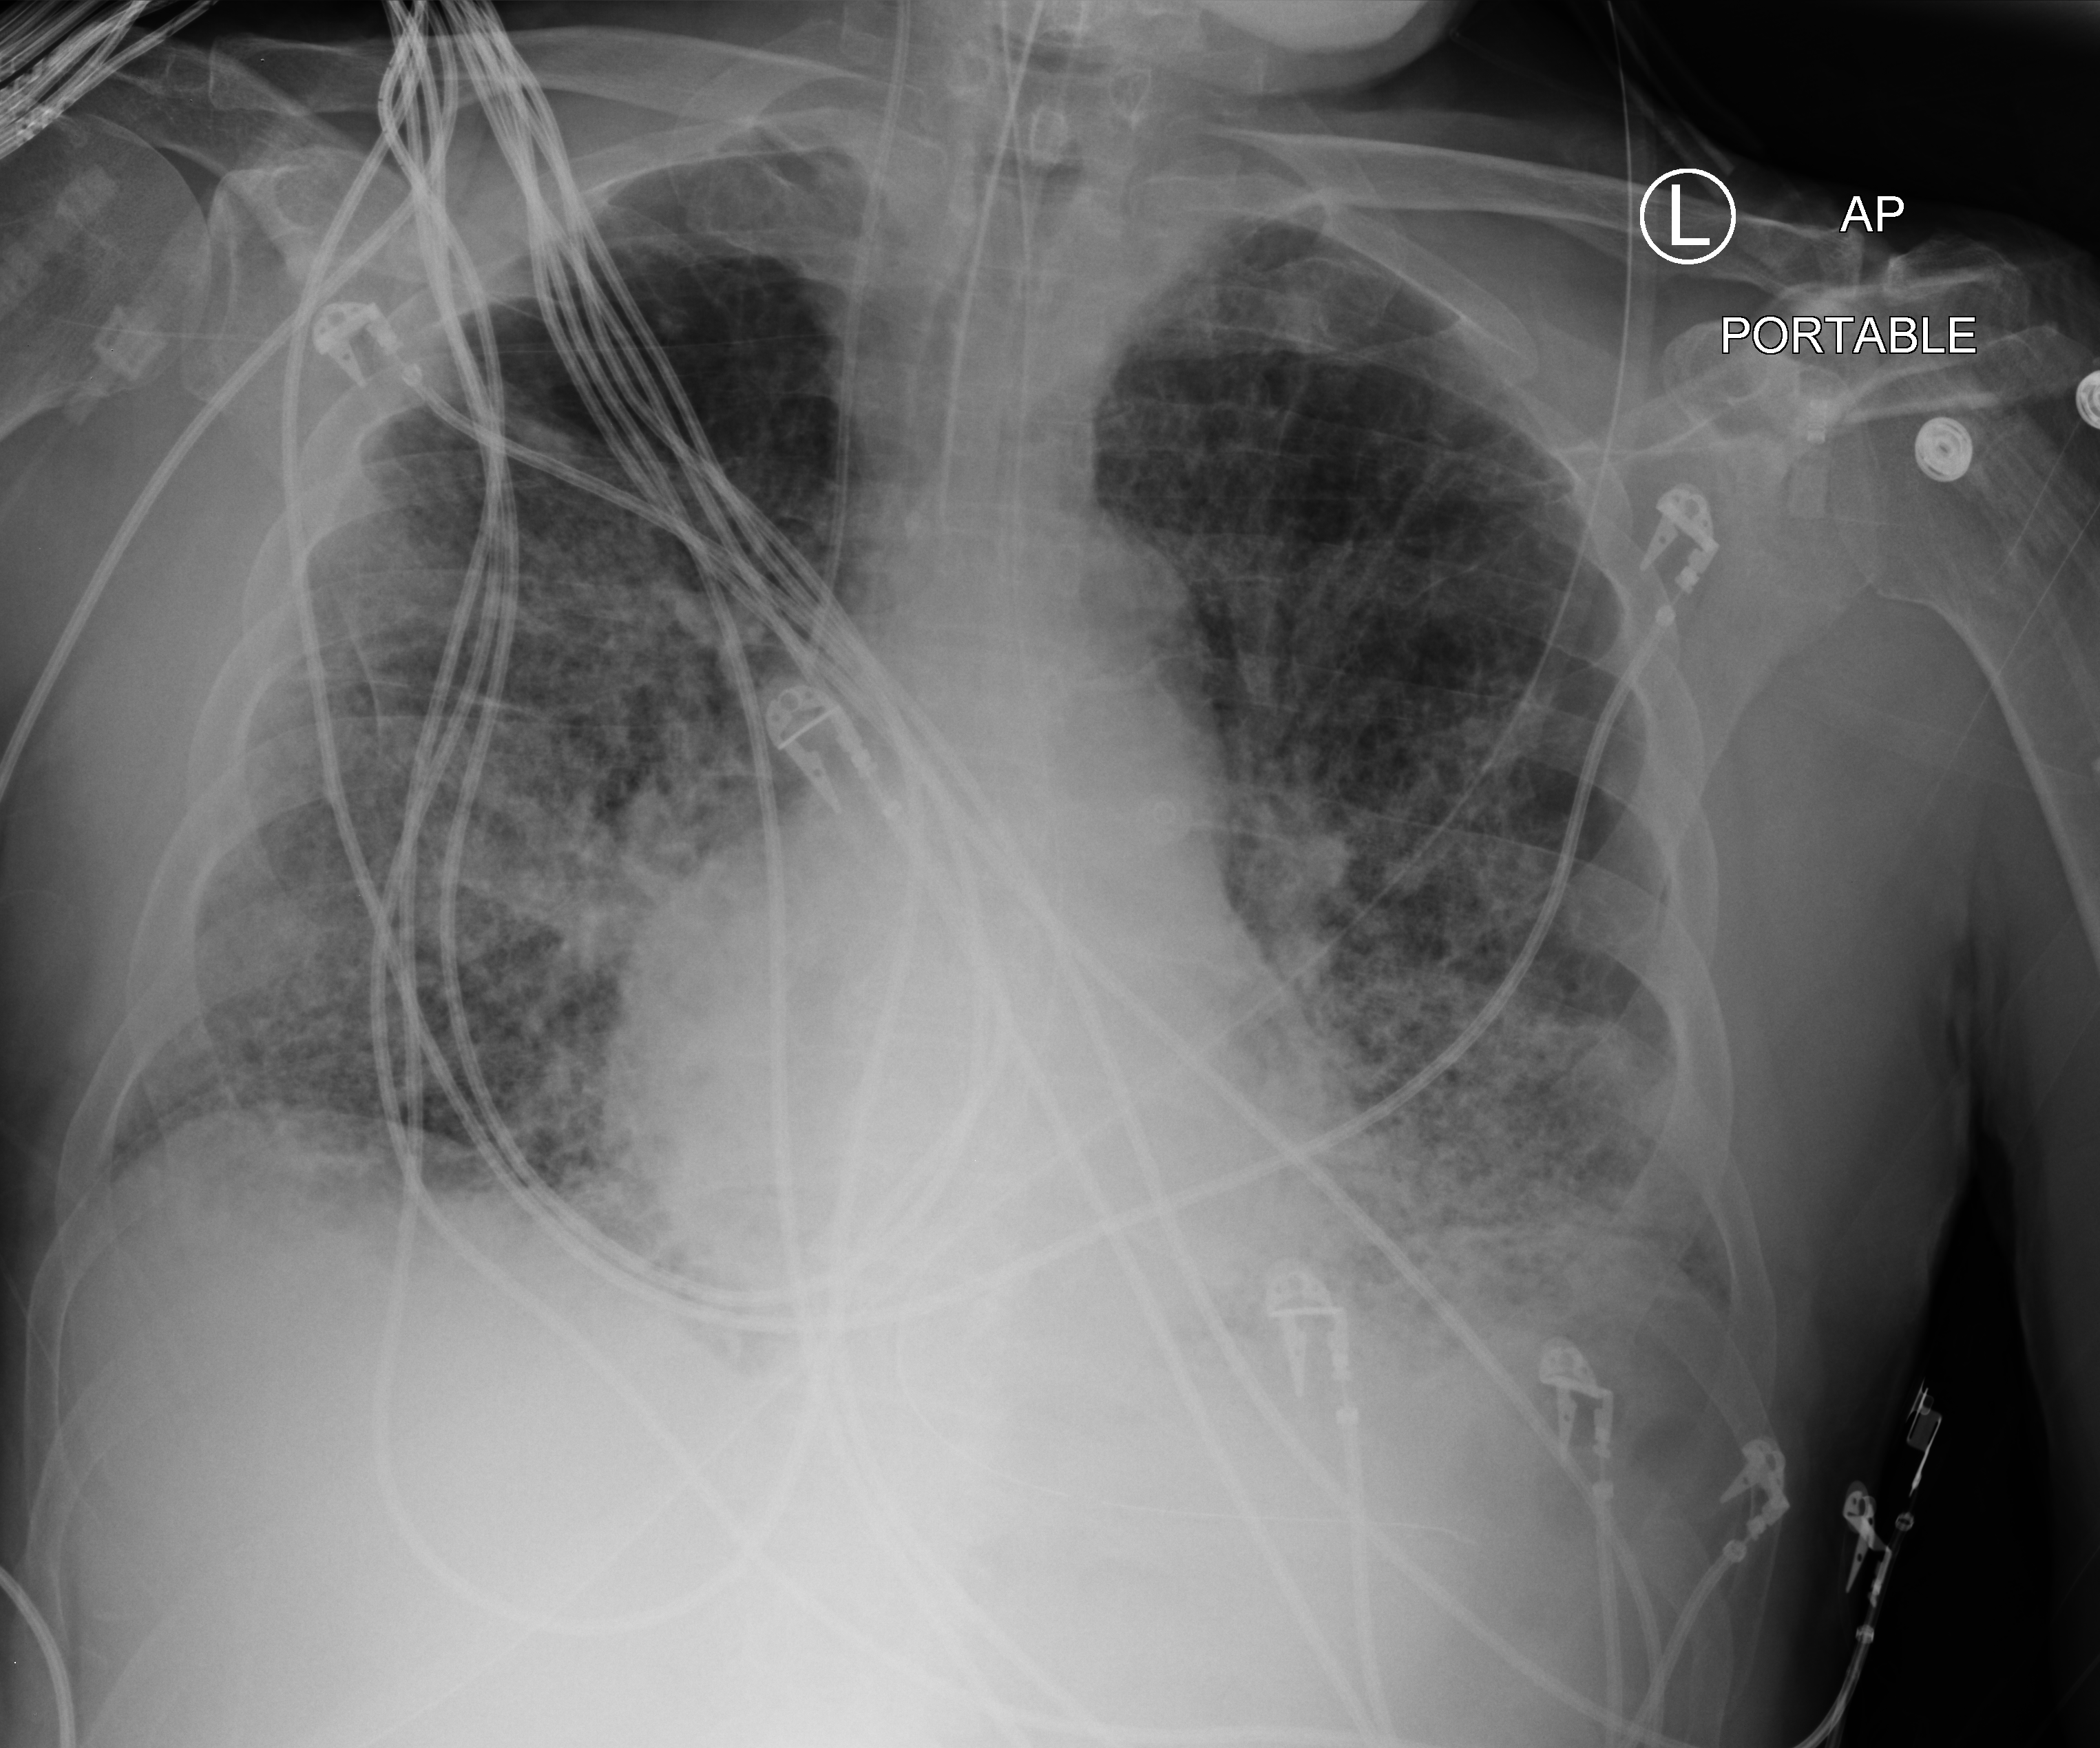
Chest X-ray (portable). Patient hospitalised with COVID-19; male, aged 75–90 years.
From the hospital-stay record, not from the radiograph (when in the stay this image was taken is not recorded): admitted to intensive care during this hospital stay: yes; mechanically ventilated during this hospital stay: yes.